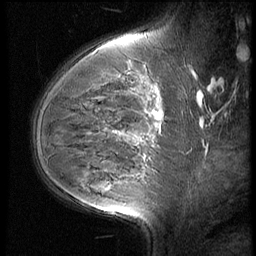
Breast MRI (dynamic contrast-enhanced), one sagittal slice; slice 40 of 60 in the series (ordered by position); 3 images stored at this slice position (order not interpretable as contrast timing); 1.5 T; TE 4.2 ms, TR 9 ms; 256 × 256 image matrix. Patient: female, 35 years. From the clinical record (not read from this slice): setting: breast cancer imaged before/during neoadjuvant chemotherapy; receptor status: HR-positive, HER2-negative.
Structures marked on this image (semi-automatic segmentation, software-assisted and operator-edited):
- analysis volume of interest (the breast-tissue region the enhancement analysis was run in; not a lesion): bounding box <56,58,176,202> (left, top, right, bottom; pixels)
- tumour enhancement mask (voxels above the 140 % enhancement threshold inside the analysis volume of interest): <154,113,160,117>